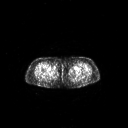
FDG PET of an extremity soft-tissue mass (from a PET/CT study), one axial slice; position 246 of 311 along the scan axis; 128 × 128 image matrix. Patient: female, 78 years. Case-level facts recorded for this patient, not image findings: histological type: leiomyosarcoma; grade: intermediate; site of the primary tumour: parascapusular.
Annotated regions visible in this slice (expert contour drawn on MRI and transferred to this co-registered scan by the dataset authors):
- gross tumour volume including surrounding oedema: bounding box (x1, y1, x2, y2) in pixels: (53, 65, 57, 69)
- gross tumour volume (mass): (53, 66, 56, 69)